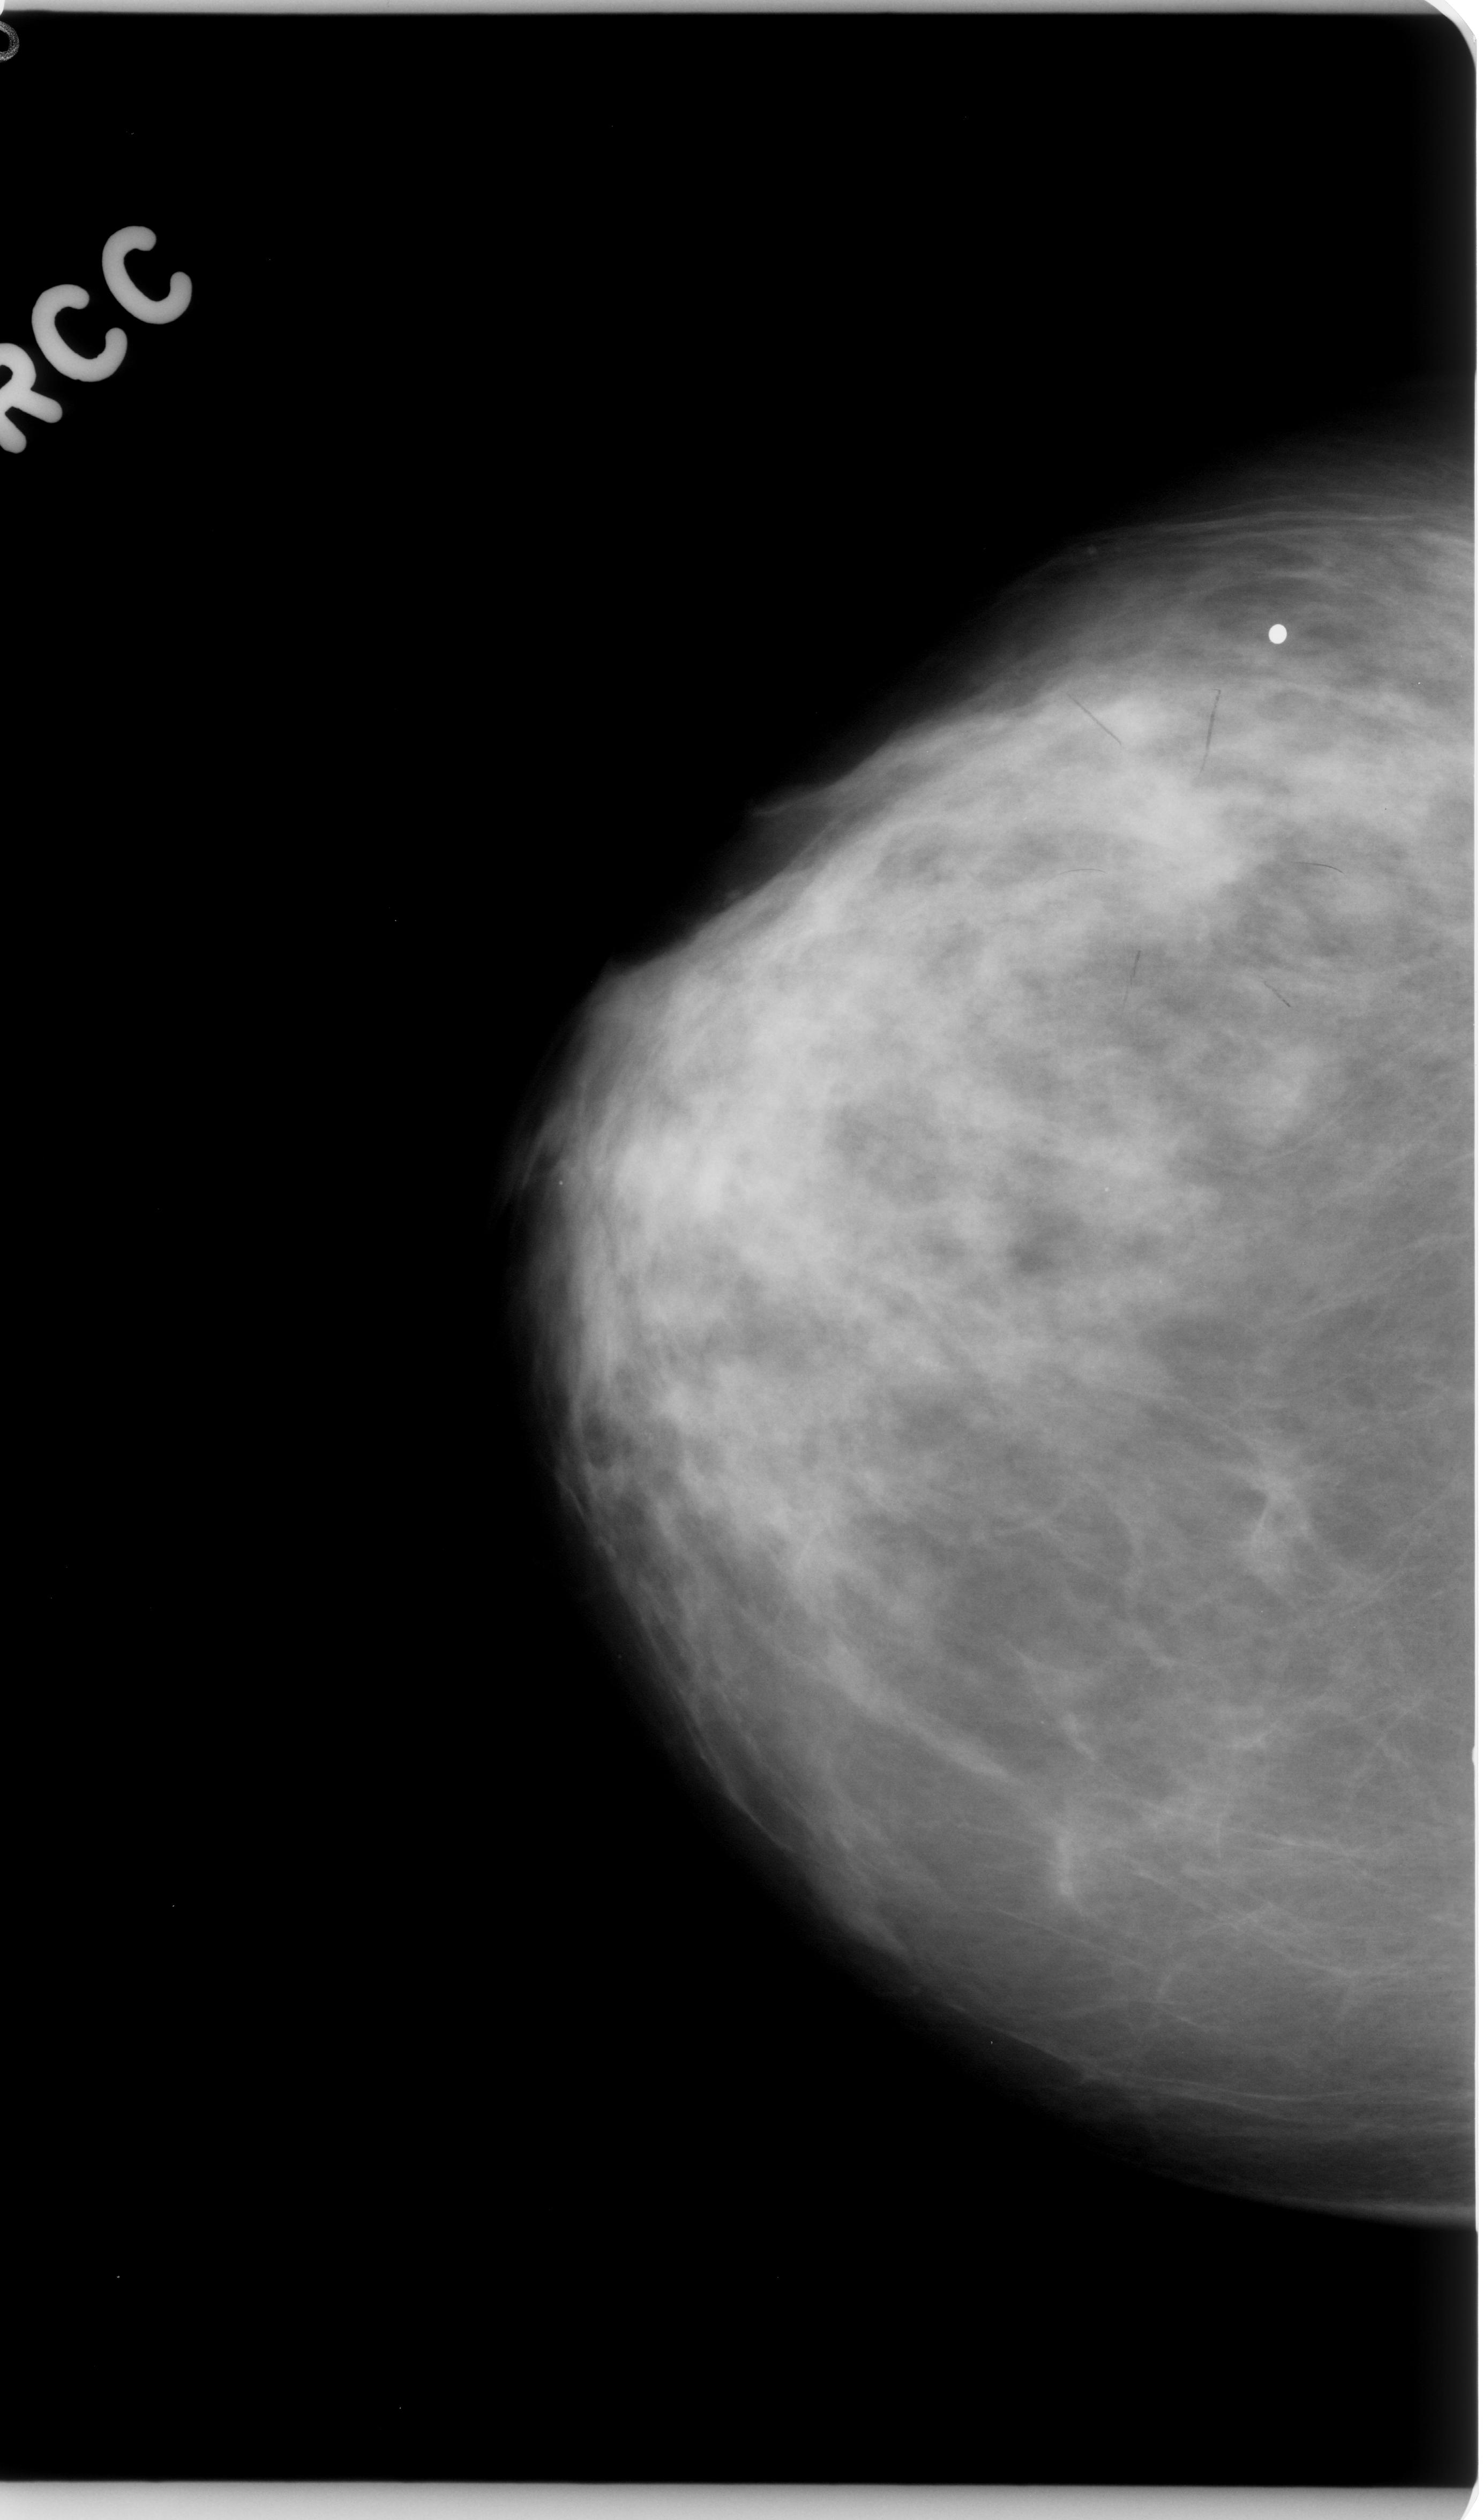
Scanned film-screen mammogram. Right breast. Craniocaudal (CC) view. 1483 × 2520 image matrix.
Expert-marked regions of interest on this film, with their recorded descriptors:
- mass, shape irregular, margins ill defined; BI-RADS assessment category 4; subtlety rating 3 on a 1 (subtle) to 5 (obvious) scale; pathology result (as recorded, not read from the image): malignant: bounding box [x1, y1, x2, y2] px = [1092, 763, 1275, 942]